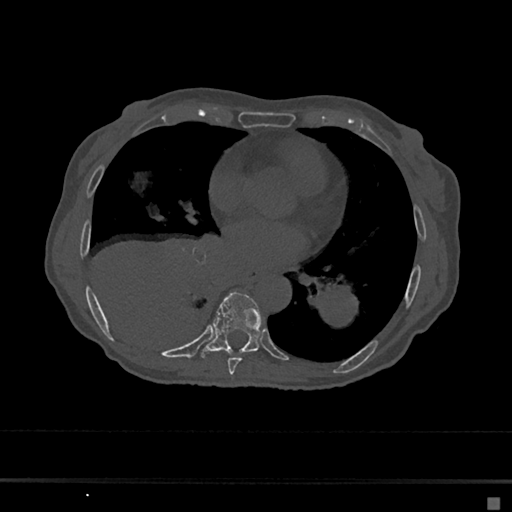
CT including the spine, one axial slice. Position 343 of 797 along the scan axis. 120 kVp. Bone window (W 1800 / L 400 HU). 512 × 512 image matrix, field of view 360 × 360 mm. Female patient, age 68 years. Case-level facts recorded for this patient, not image findings: primary cancer: renal.
Outlined on this slice (semi-automatic segmentation, software-assisted and operator-edited):
- T7 vertebra: bounding box [x1, y1, x2, y2] px = [228, 358, 242, 375]
- T8 vertebra: [201, 291, 262, 358]